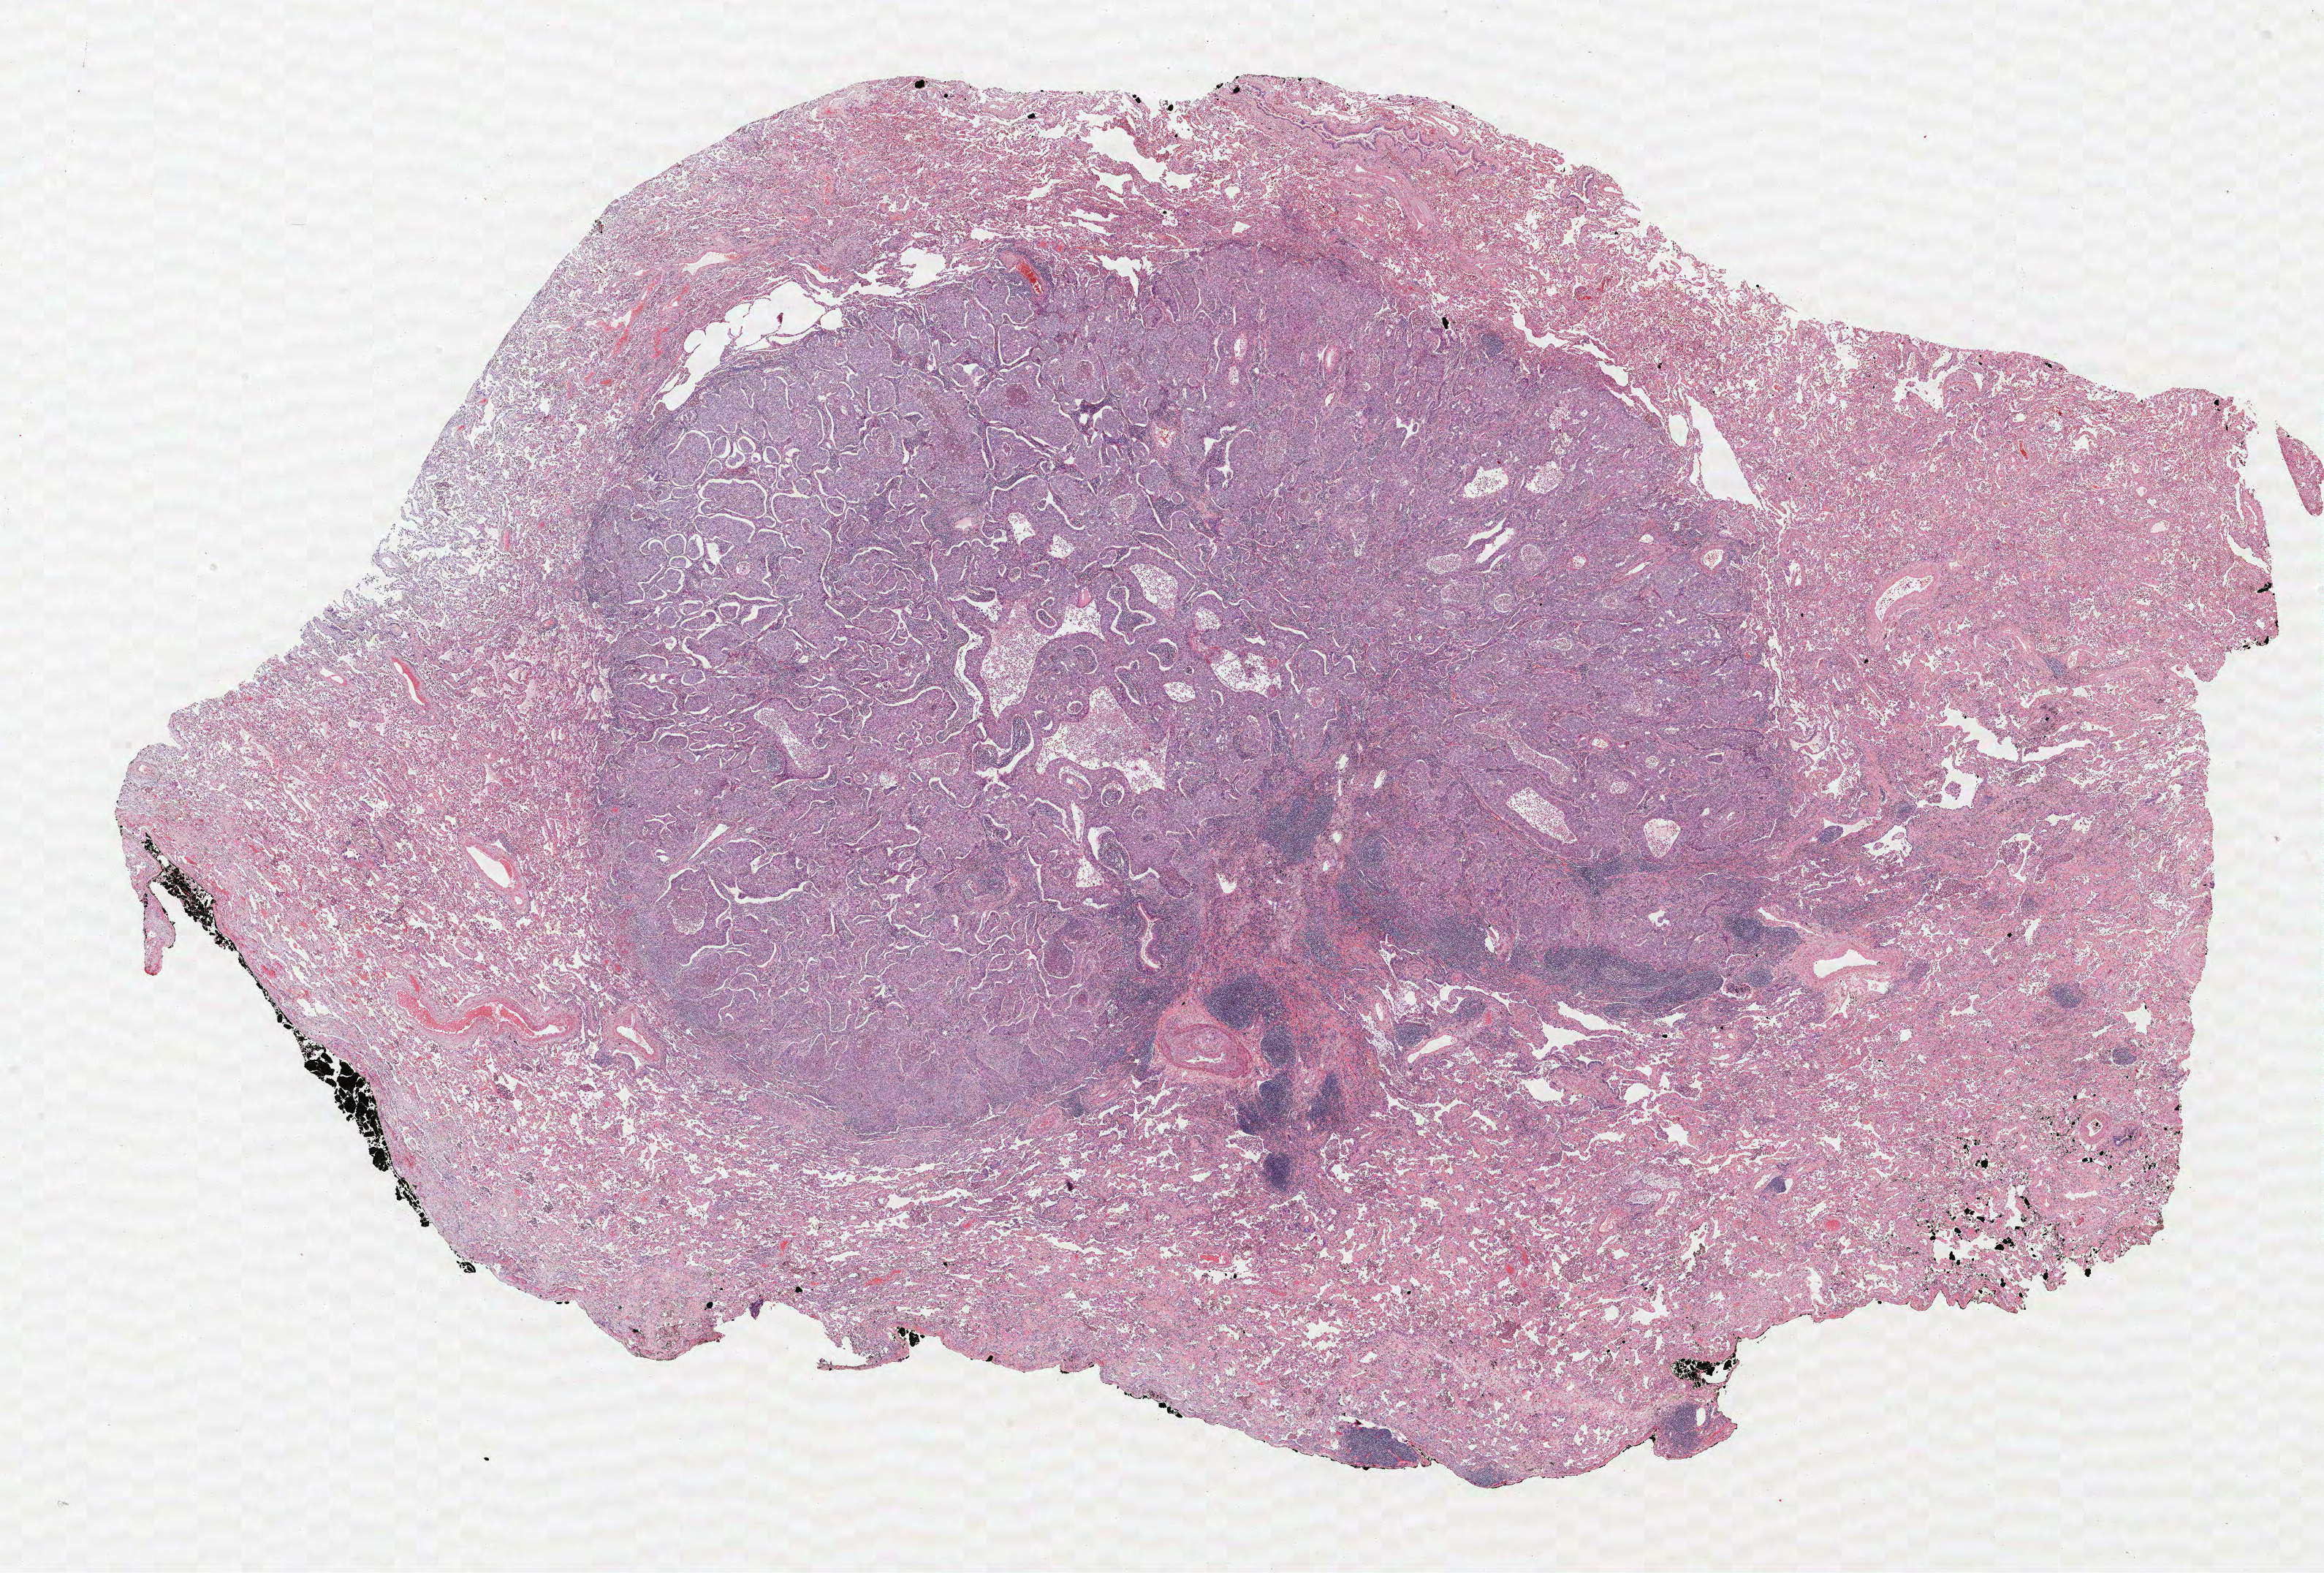
Whole-slide histology image, H&E-stained — shown as a low-resolution overview of the whole scanned area (about 25.4 x 17.2 mm). Formalin-fixed paraffin-embedded (FFPE) section. Lung. Female, age 56 at enrolment. Current smoker at enrolment. Grade: poorly differentiated (G3).
- stage (AJCC 6th edition): IA
- primary tumour location (clinical record): right lower lobe
- participant's lung-cancer diagnosis: Adenocarcinoma, NOS
- tumour size (pathology): 12 mm